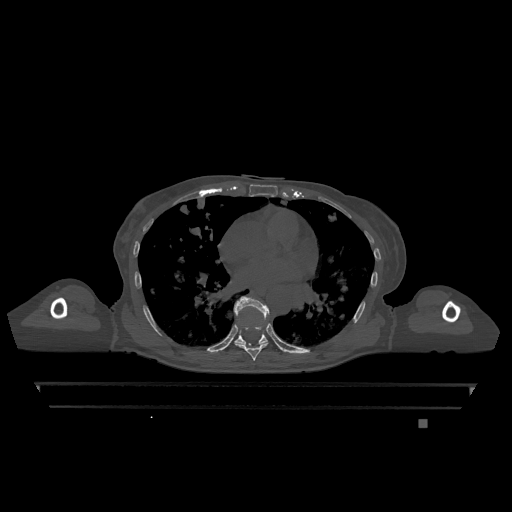
CT including the spine, one axial slice; slice 718 of 1317 in the series (ordered by position); bone window (W 1800 / L 400 HU); 512 × 512 image matrix, field of view 500 × 500 mm. Female patient, age 74 years. From the clinical record (not read from this slice): primary cancer: lung; vertebrae with lytic lesions (as recorded): T1, T4, T5, T6, L4, L5.
Outlined on this slice (semi-automatically segmented with operator editing):
- T7 vertebra: bounding box (x1, y1, x2, y2) in pixels: (235, 343, 268, 361)
- T9 vertebra: (234, 297, 270, 345)